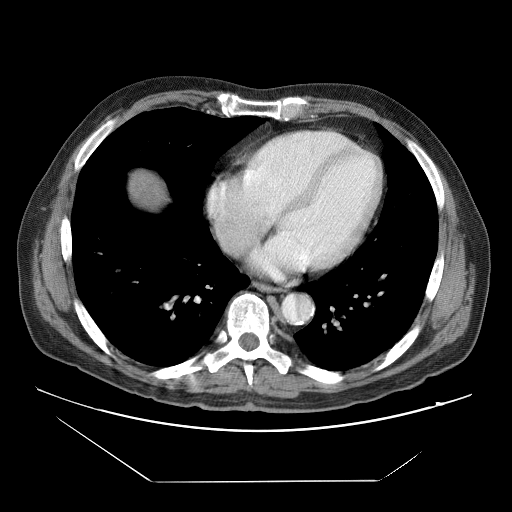
Contrast-enhanced abdominal CT (liver protocol), one axial slice; slice 77 of 83 in the series (ordered by position); soft-tissue window (W 400 / L 40 HU); 2.5 mm slice thickness; 512 × 512 image matrix, field of view 420 × 420 mm. From the clinical record (not read from this slice): diagnosis: hepatocellular carcinoma (patient treated with transarterial chemoembolisation; whether this scan precedes or follows treatment is not stated here); TNM stage (as recorded): Stage-IVB; Child-Pugh class: B.
Structures marked on this image (semi-automatic segmentation, software-assisted and operator-edited):
- liver parenchyma outside the tumour (the mass and vessels are separate outlines, so this box may not span the whole liver): bounding box [x1, y1, x2, y2] px = [129, 172, 166, 208]